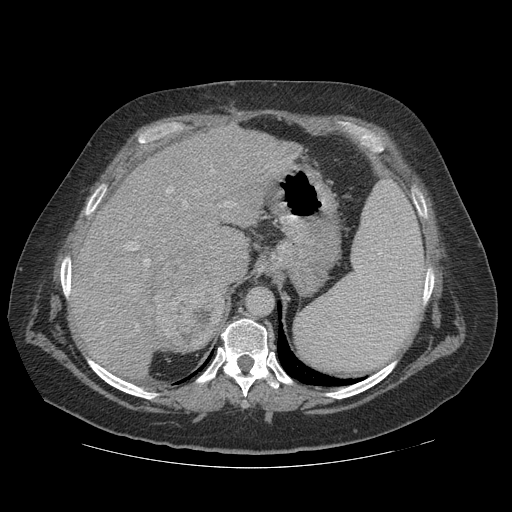
Contrast-enhanced abdominal CT (liver protocol), one axial slice; reconstruction kernel STANDARD; 140 kVp; soft-tissue window (W 400 / L 40 HU); 2.5 mm slice thickness; 512 × 512 image matrix, field of view 420 × 420 mm. Case-level facts recorded for this patient, not image findings: diagnosis: hepatocellular carcinoma (patient treated with transarterial chemoembolisation; whether this scan precedes or follows treatment is not stated here); TNM stage (as recorded): Stage-IIIA.
Outlined on this slice (semi-automatically segmented with operator editing):
- liver parenchyma outside the tumour (the mass and vessels are separate outlines, so this box may not span the whole liver): bounding box (x1, y1, x2, y2) in pixels: (70, 124, 302, 376)
- mass: (131, 258, 224, 353)
- liver vessels: (94, 166, 267, 330)